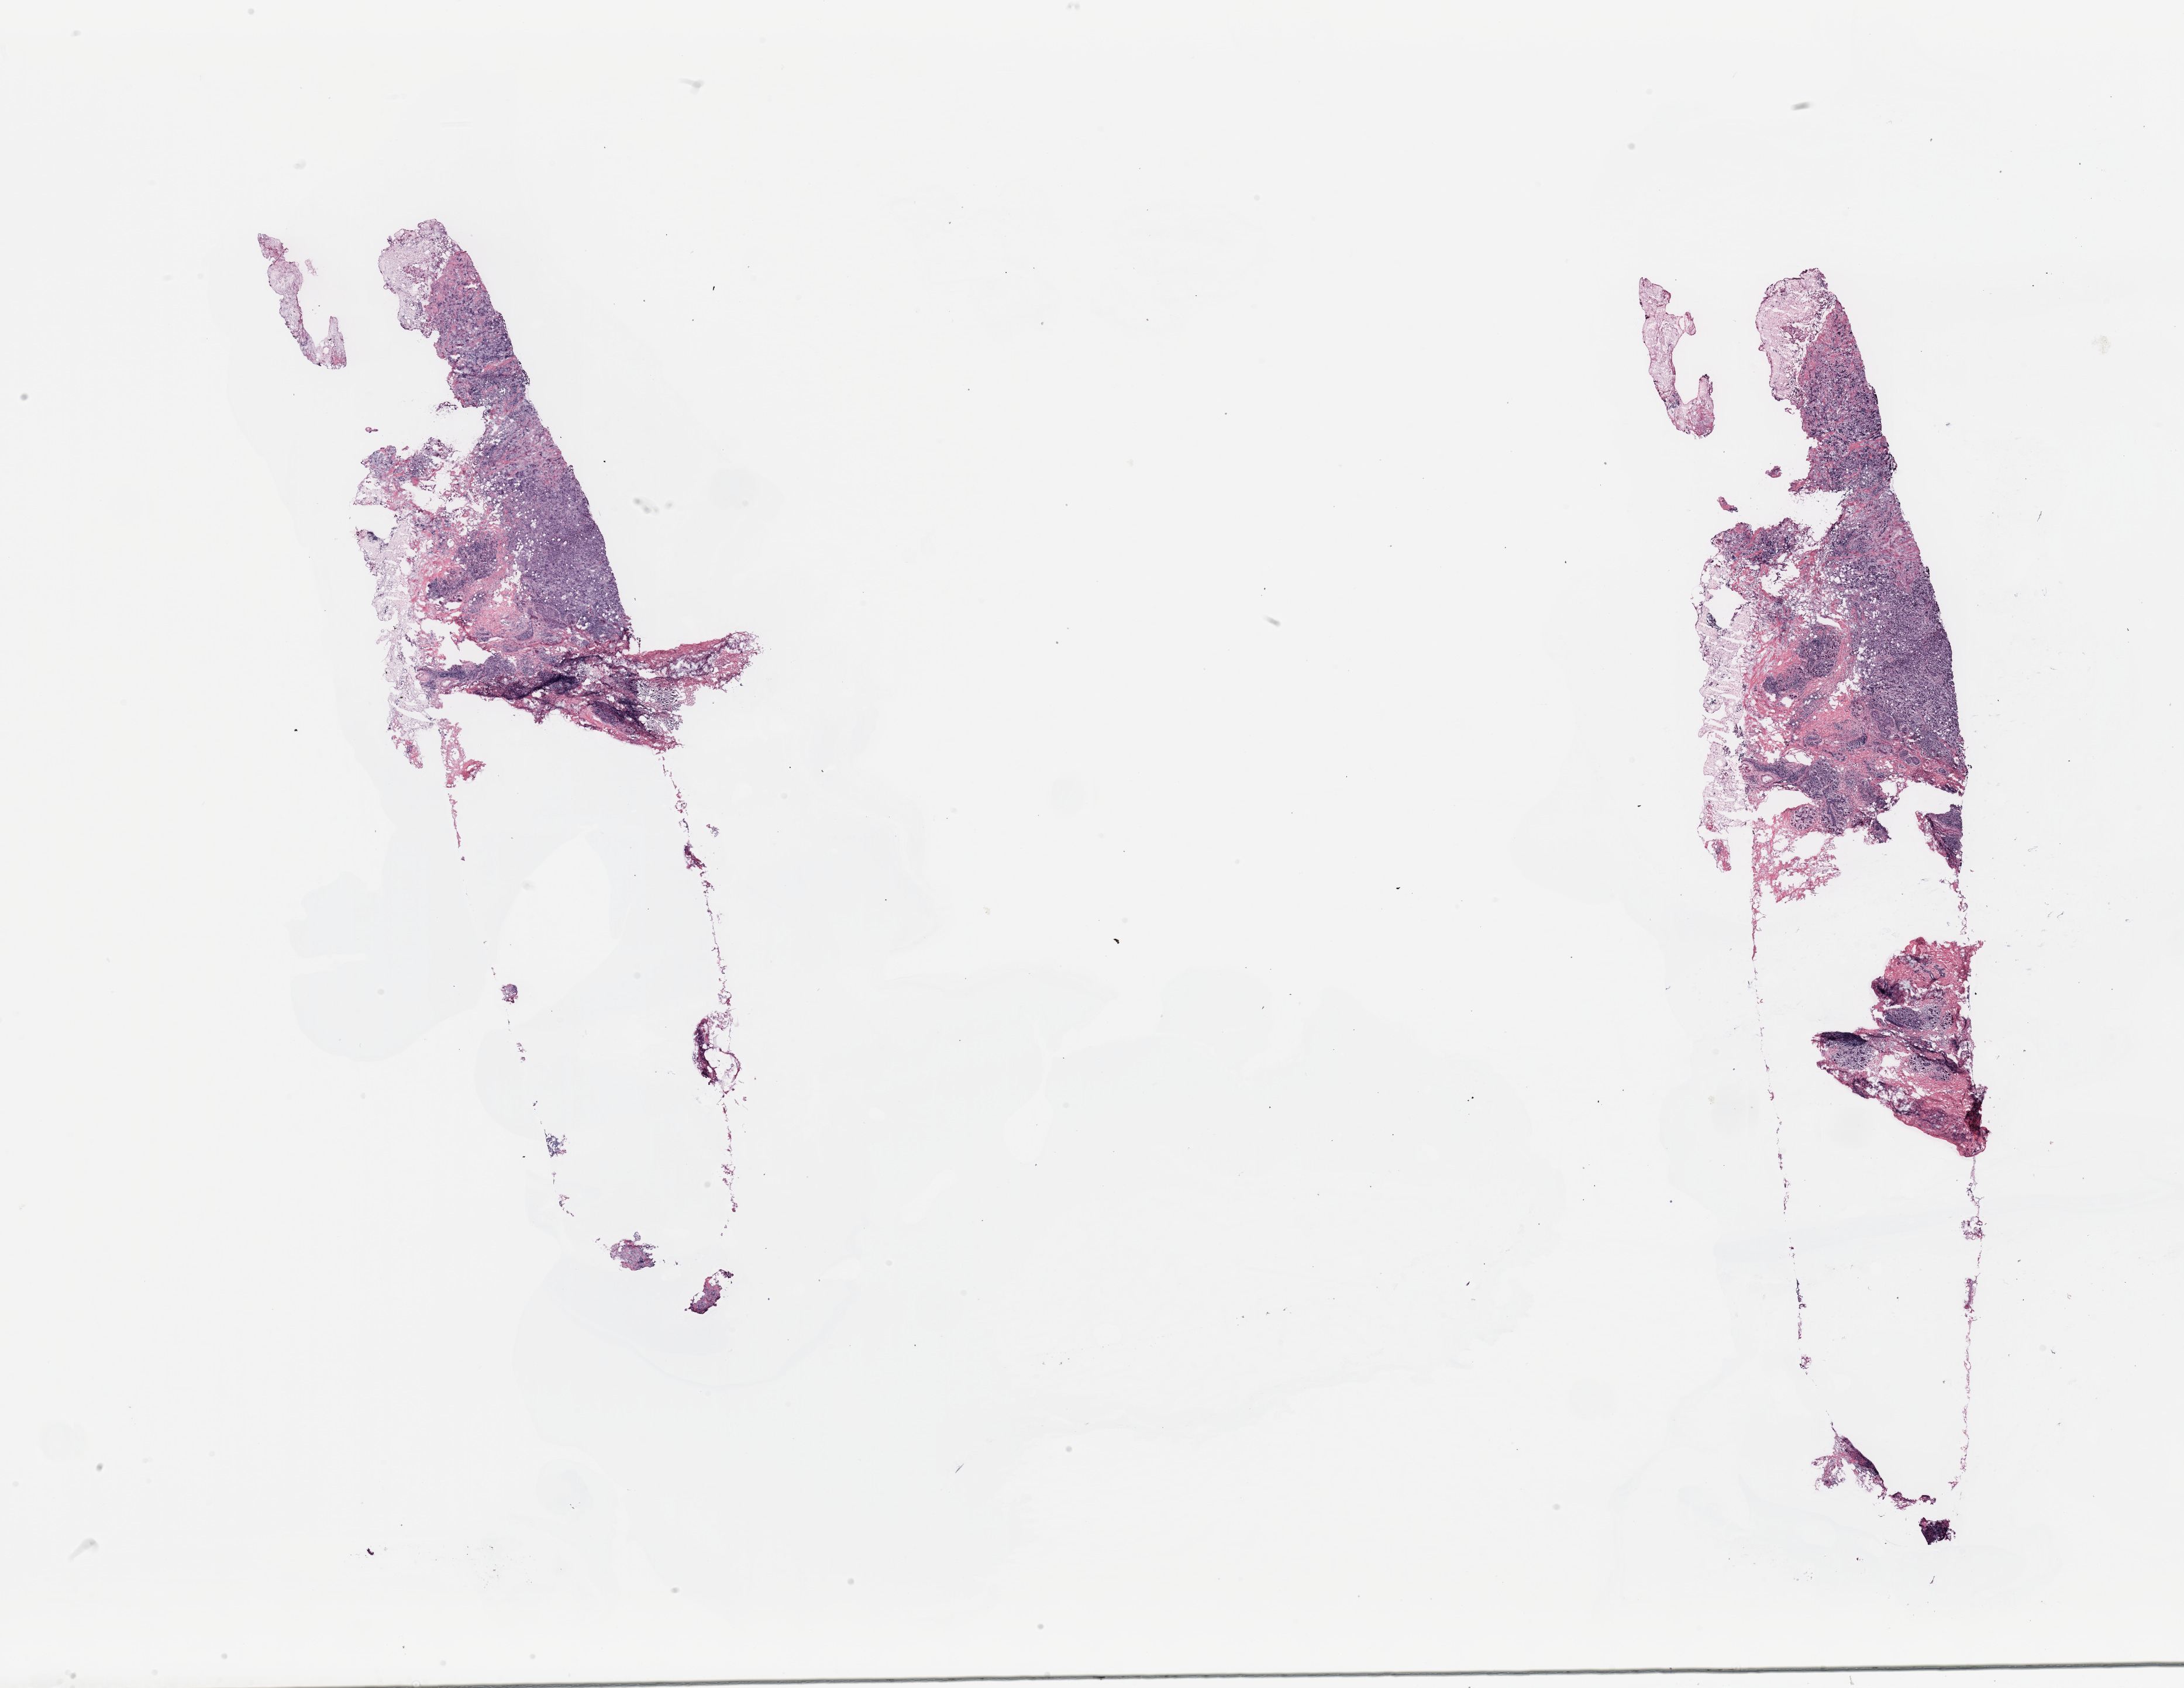
H&E-stained whole-slide image, a low-resolution overview of the entire scanned area, about 29.5 x 22.8 mm (from a 20x scan). Breast, tissue type not recorded.
• patient diagnosis (cohort enrolment): breast cancer (breast)